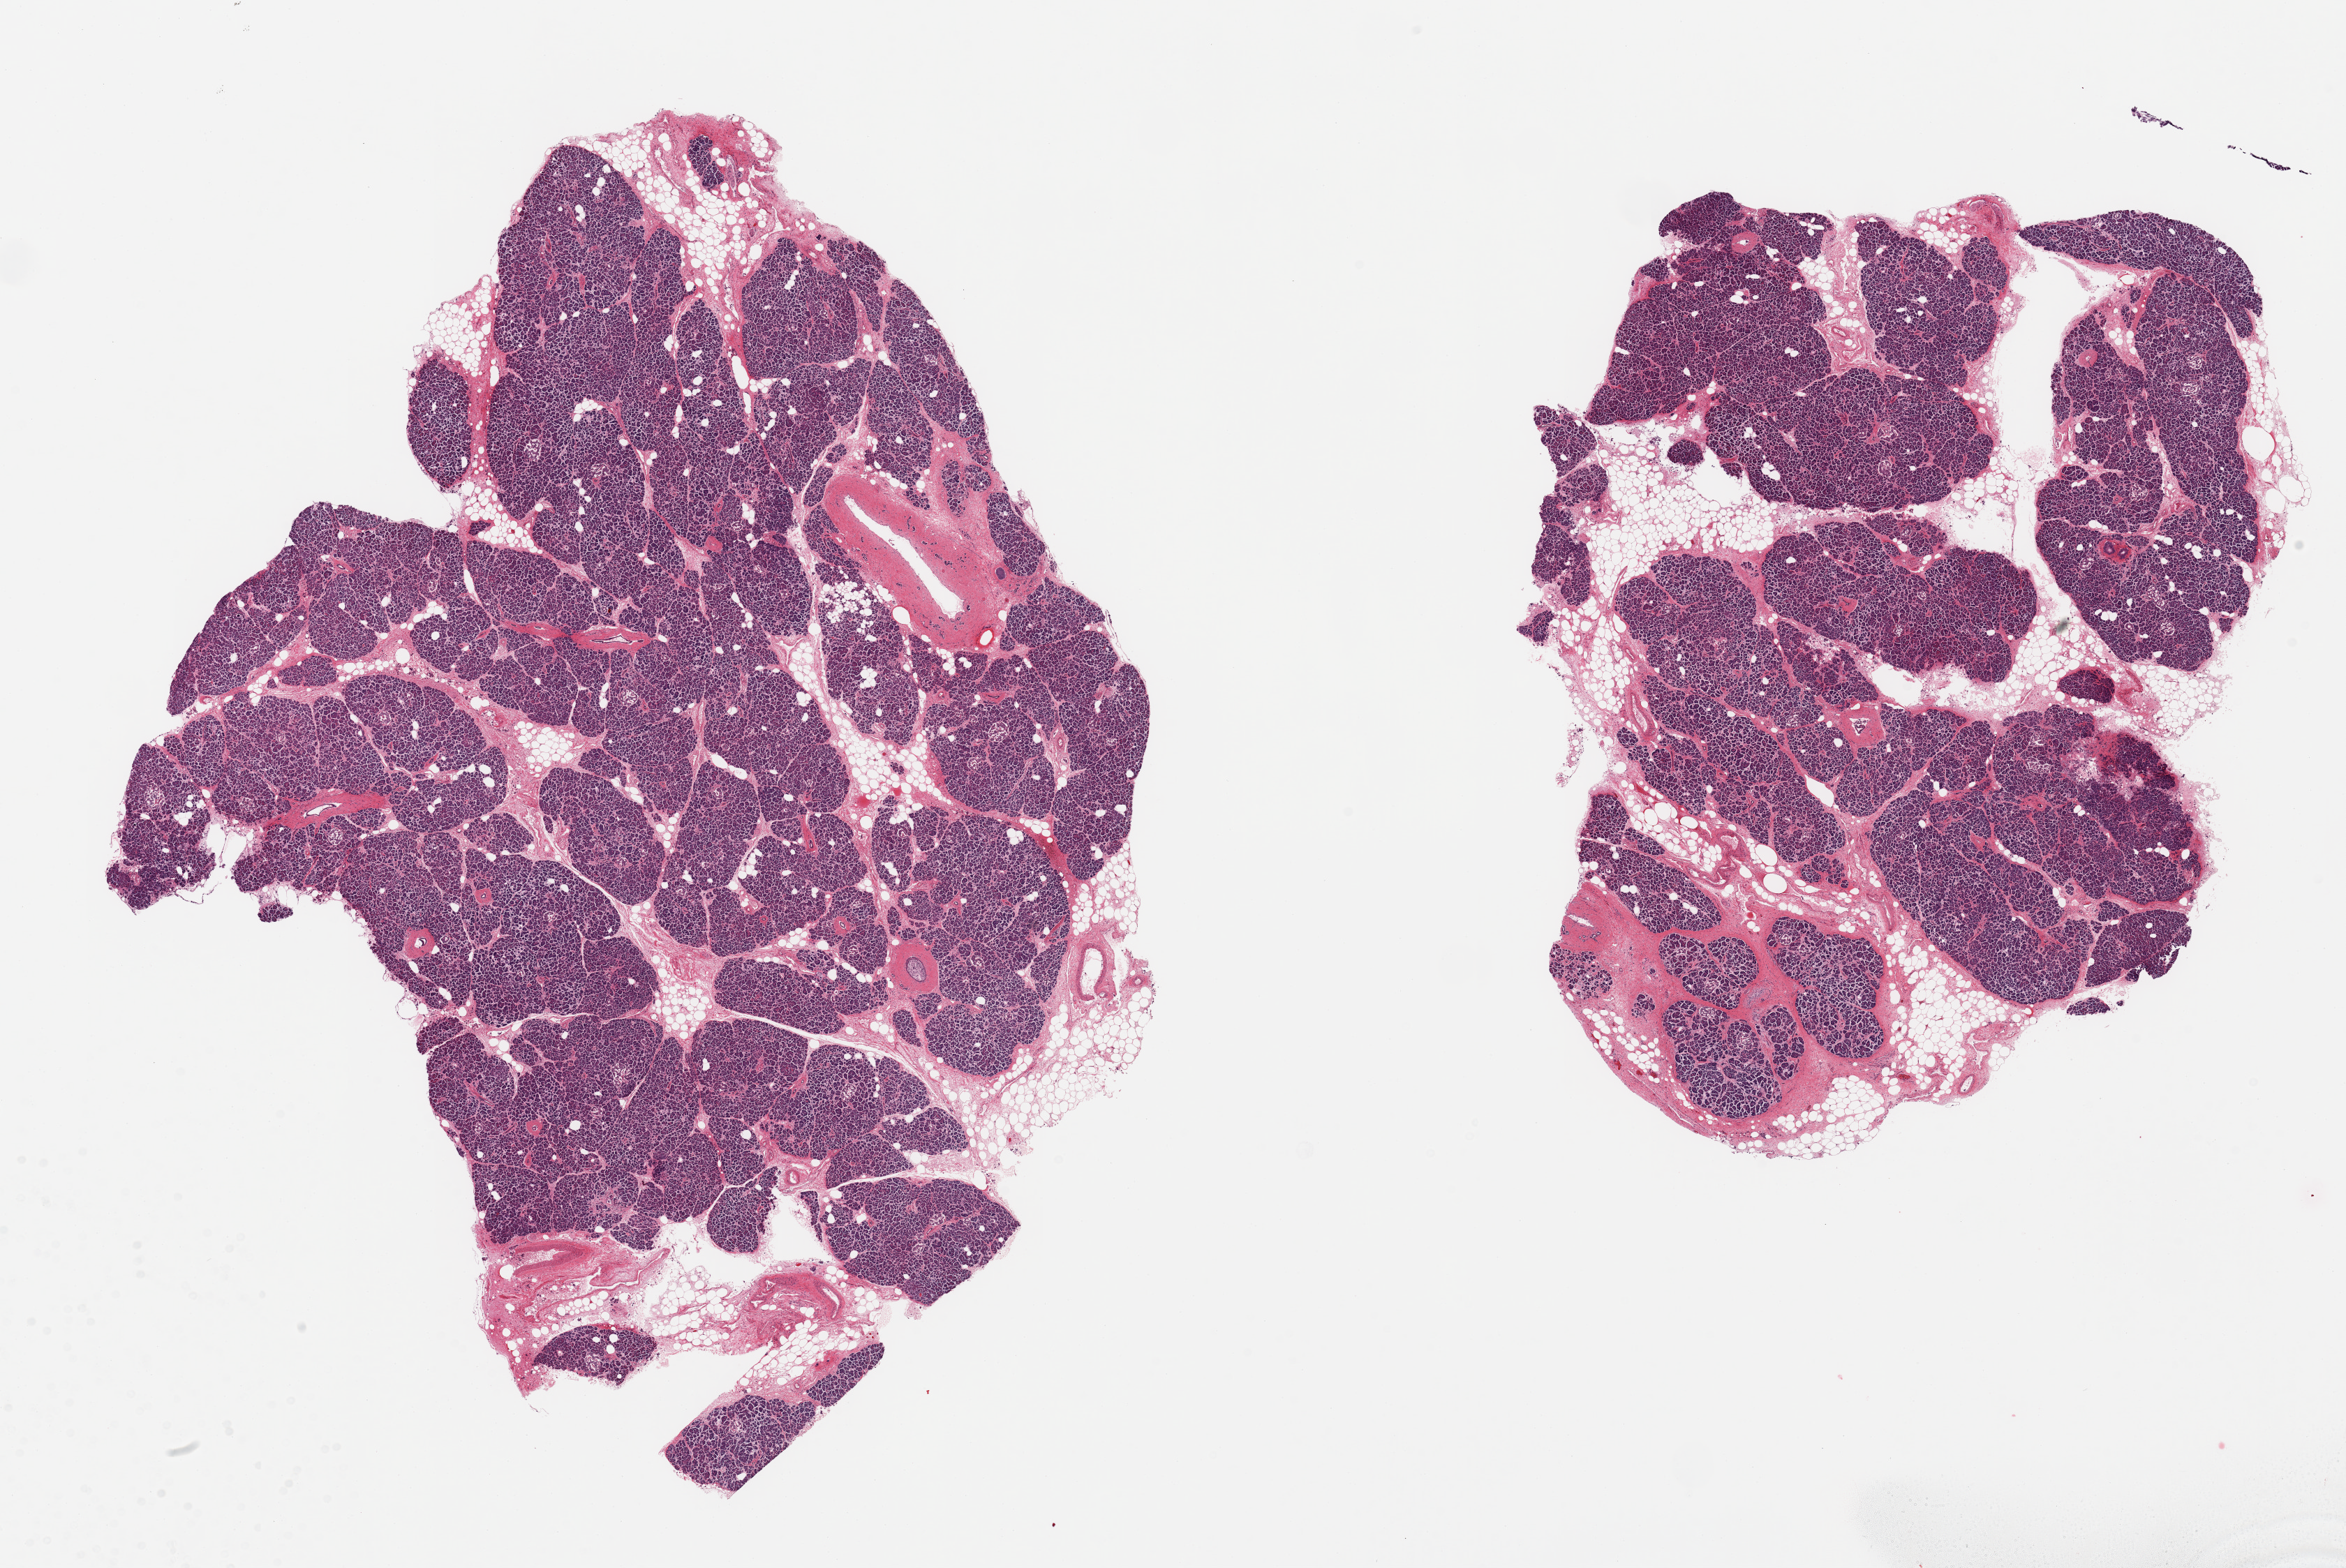
H&E whole-slide image, shown as a low-resolution overview of the whole scanned area (about 26.6 x 17.8 mm); PAXgene-fixed paraffin-embedded (PFPE) section; section of pancreas (target tissue); donor tissue sample. Female donor.
Review note (as recorded): 2 pieces; 20% internal fat.